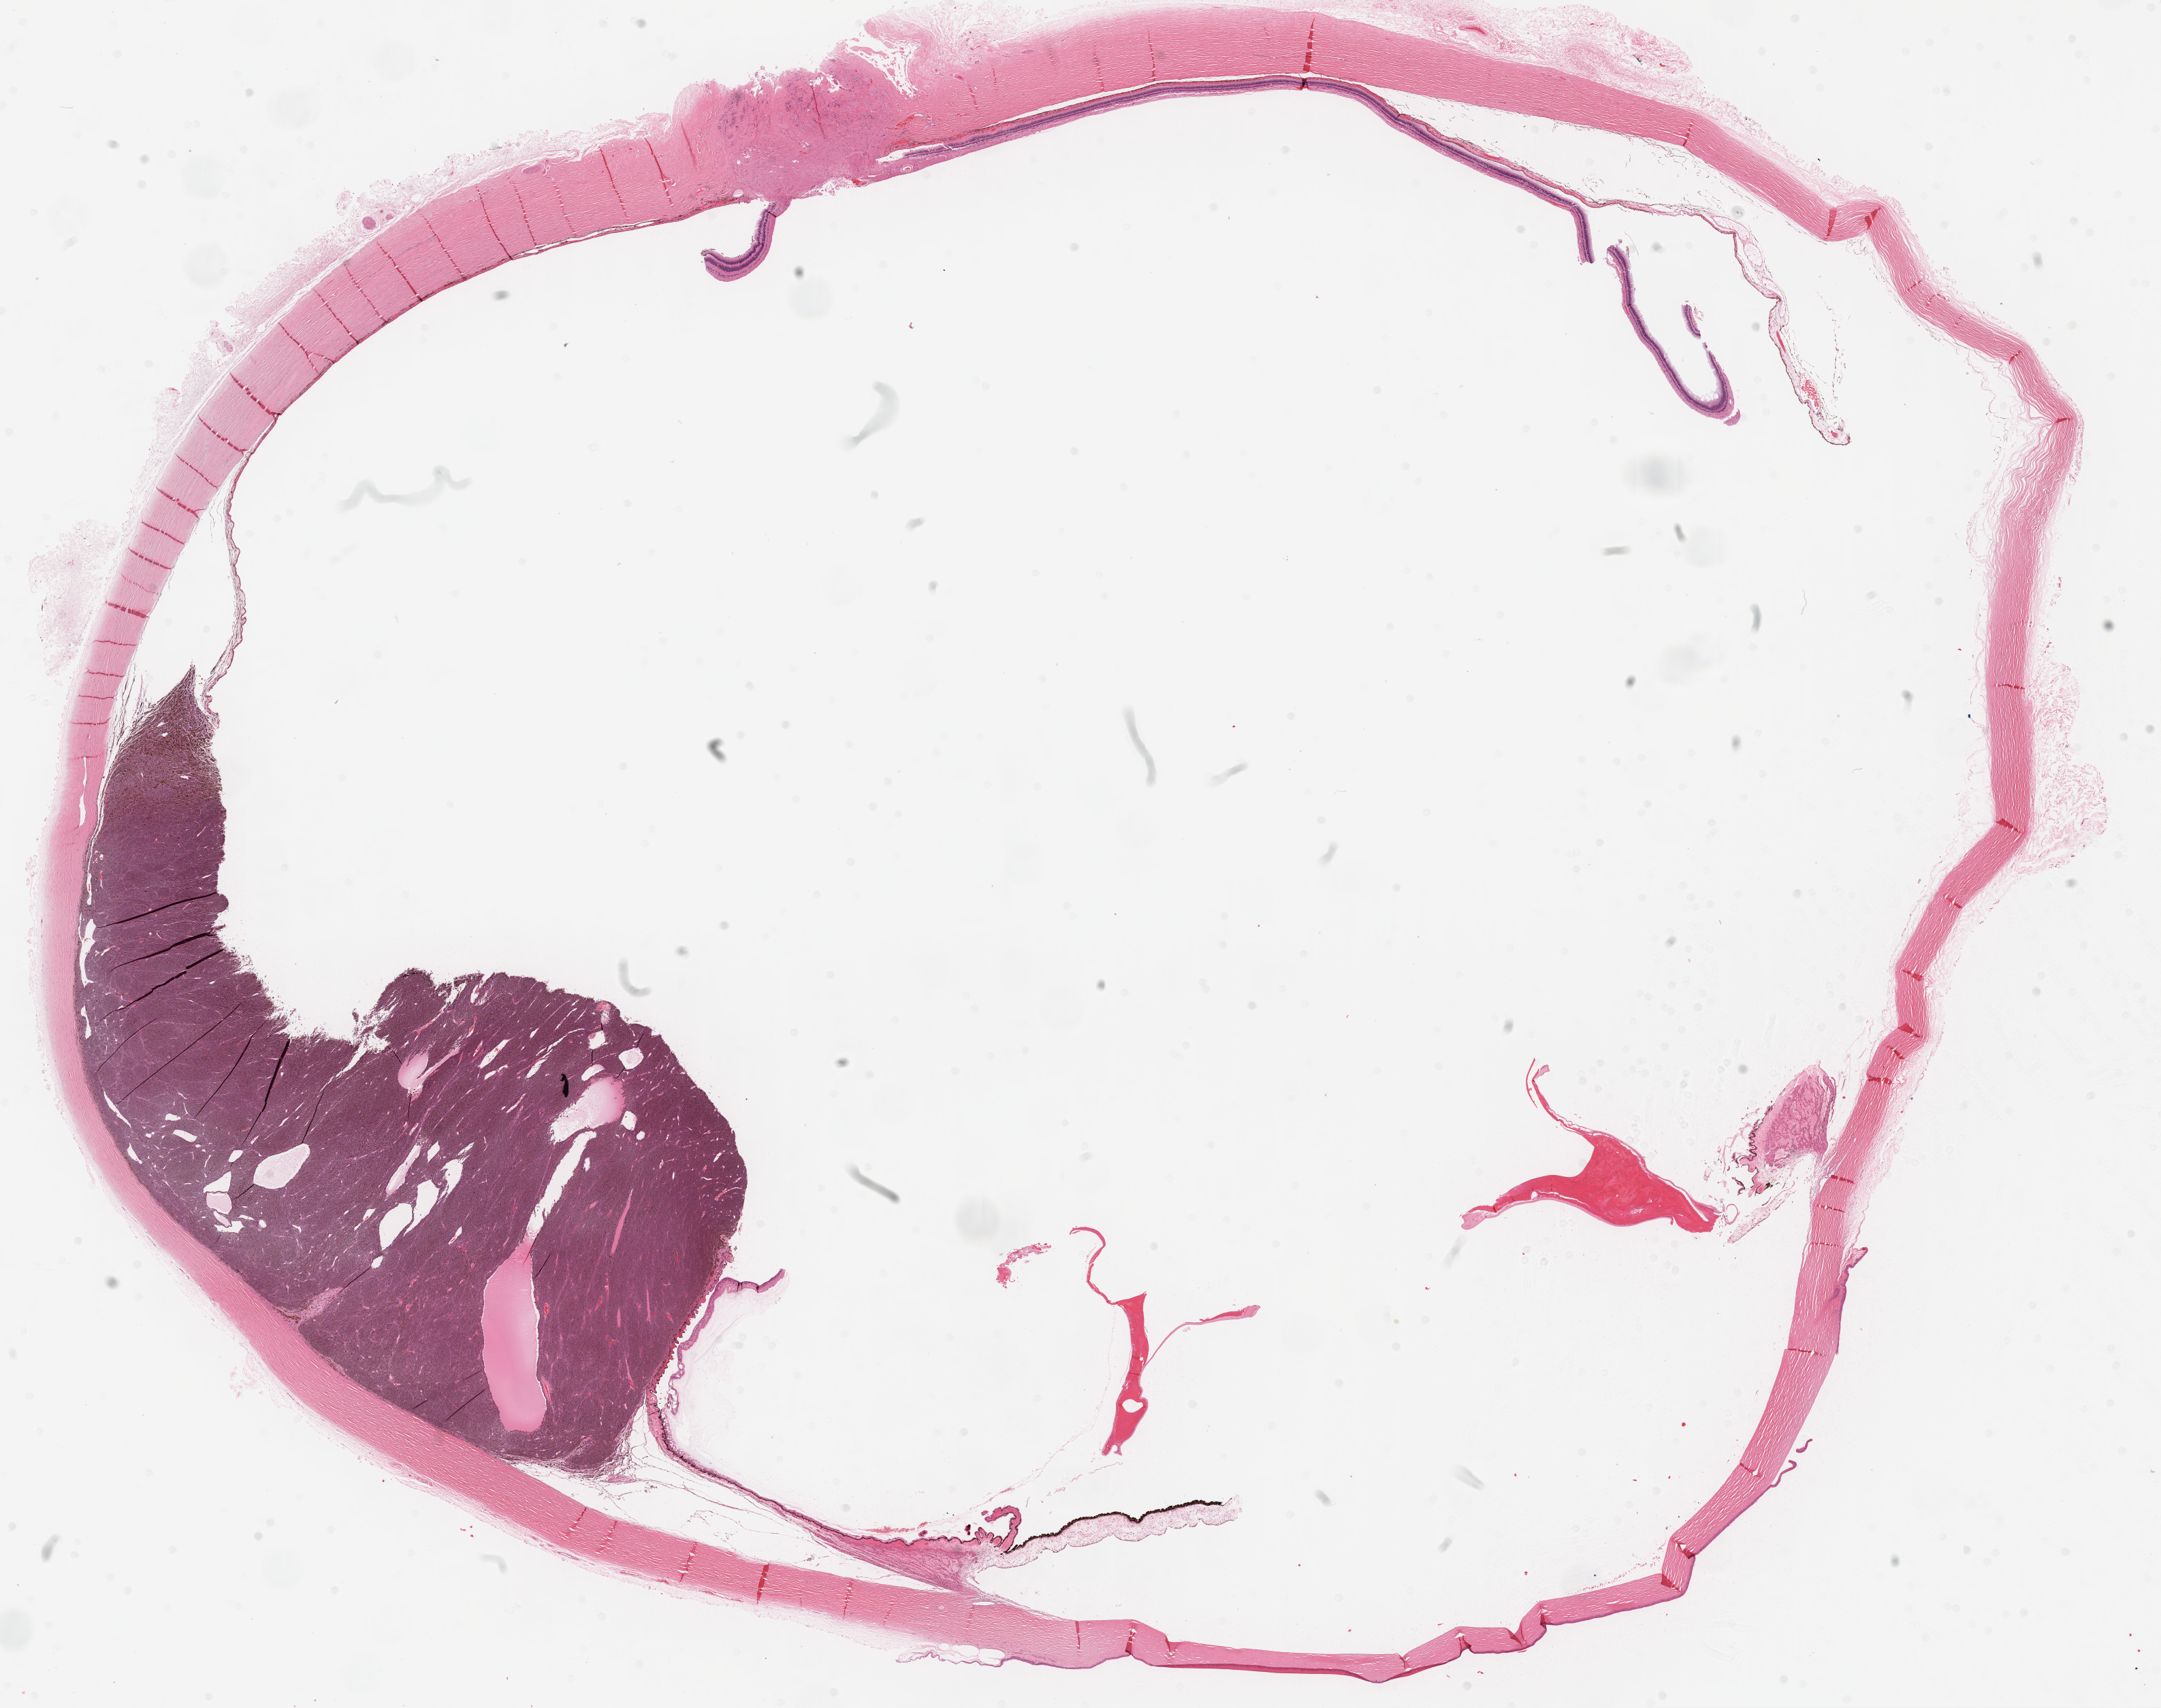
Whole-slide histology image, H&E, low-resolution overview of the scanned area, about 25.6 x 20.2 mm (acquisition: 20x scan). Formalin-fixed paraffin-embedded (FFPE) diagnostic section. Sample: primary tumour, uvea. Female, age 64 years at initial diagnosis.
- pathologic diagnosis: Spindle cell melanoma, type B (choroid)
- AJCC pathologic stage: IIB